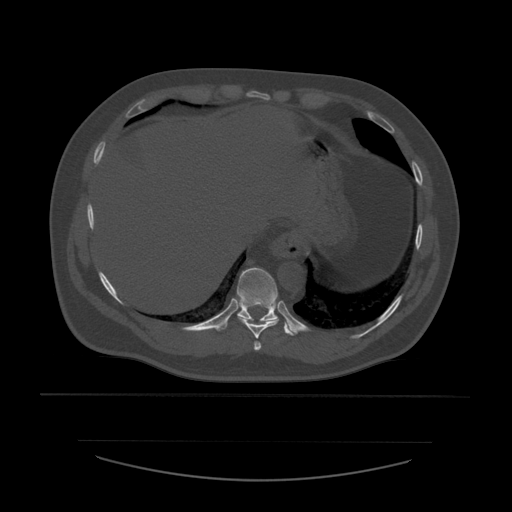
CT including the spine, one axial slice. Slice 308 of 532 in the series (ordered by position). Reconstruction kernel STANDARD. 120 kVp. Bone window (W 1800 / L 400 HU). 512 × 512 image matrix, field of view 441 × 441 mm. Patient age 44 years. From the clinical record (not read from this slice): primary cancer: soft tissue sarcoma.
Outlined on this slice (semi-automatic segmentation, software-assisted and operator-edited):
- T10 vertebra: bounding box <218,268,296,336> (left, top, right, bottom; pixels)
- T8 vertebra: <254,341,262,352>
- T9 vertebra: <238,268,280,339>